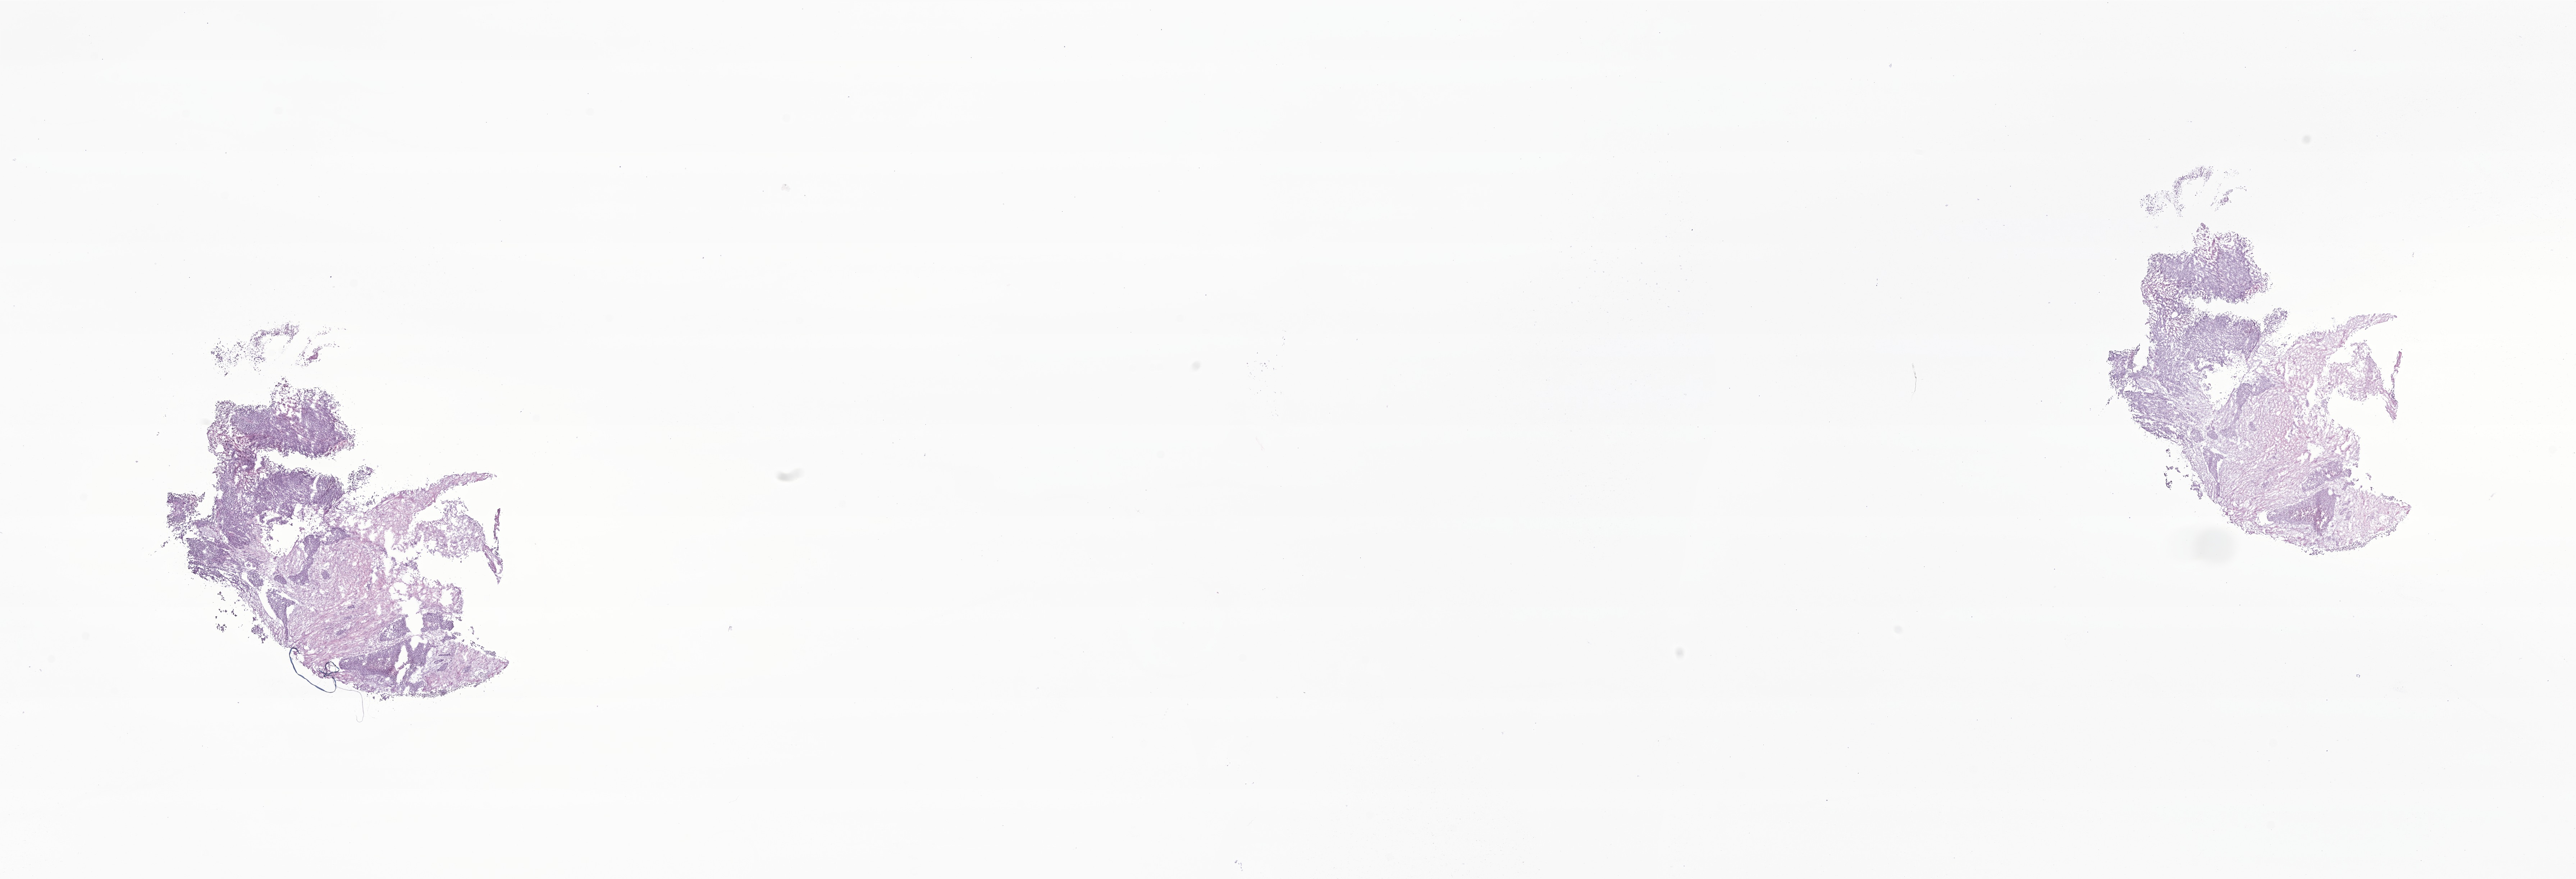
Haematoxylin and eosin whole-slide image of tumor tissue from the abdomen — low-resolution overview of the scanned area, about 30.2 x 10.3 mm. Frozen section (OCT-embedded). Patient female; age 119 months (9 years 11 months).
Recorded diagnosis: Neoplasm, uncertain whether benign or malignant.